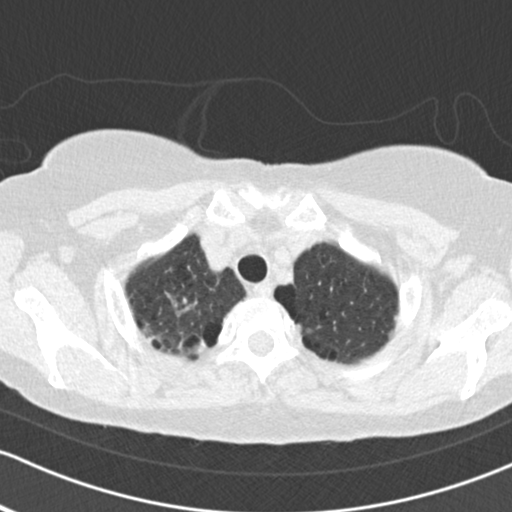
Low-dose screening chest CT, one axial slice; position 146 of 161 along the scan axis; reconstruction kernel B30f; lung window (W 1500 / L -600 HU); 2 mm slice thickness; 512 × 512 image matrix.
Outlined on this slice (manually delineated by an expert):
- lesion 1 (tumor, upper lobe of right lung): bounding box [x1, y1, x2, y2] px = [194, 338, 207, 353]